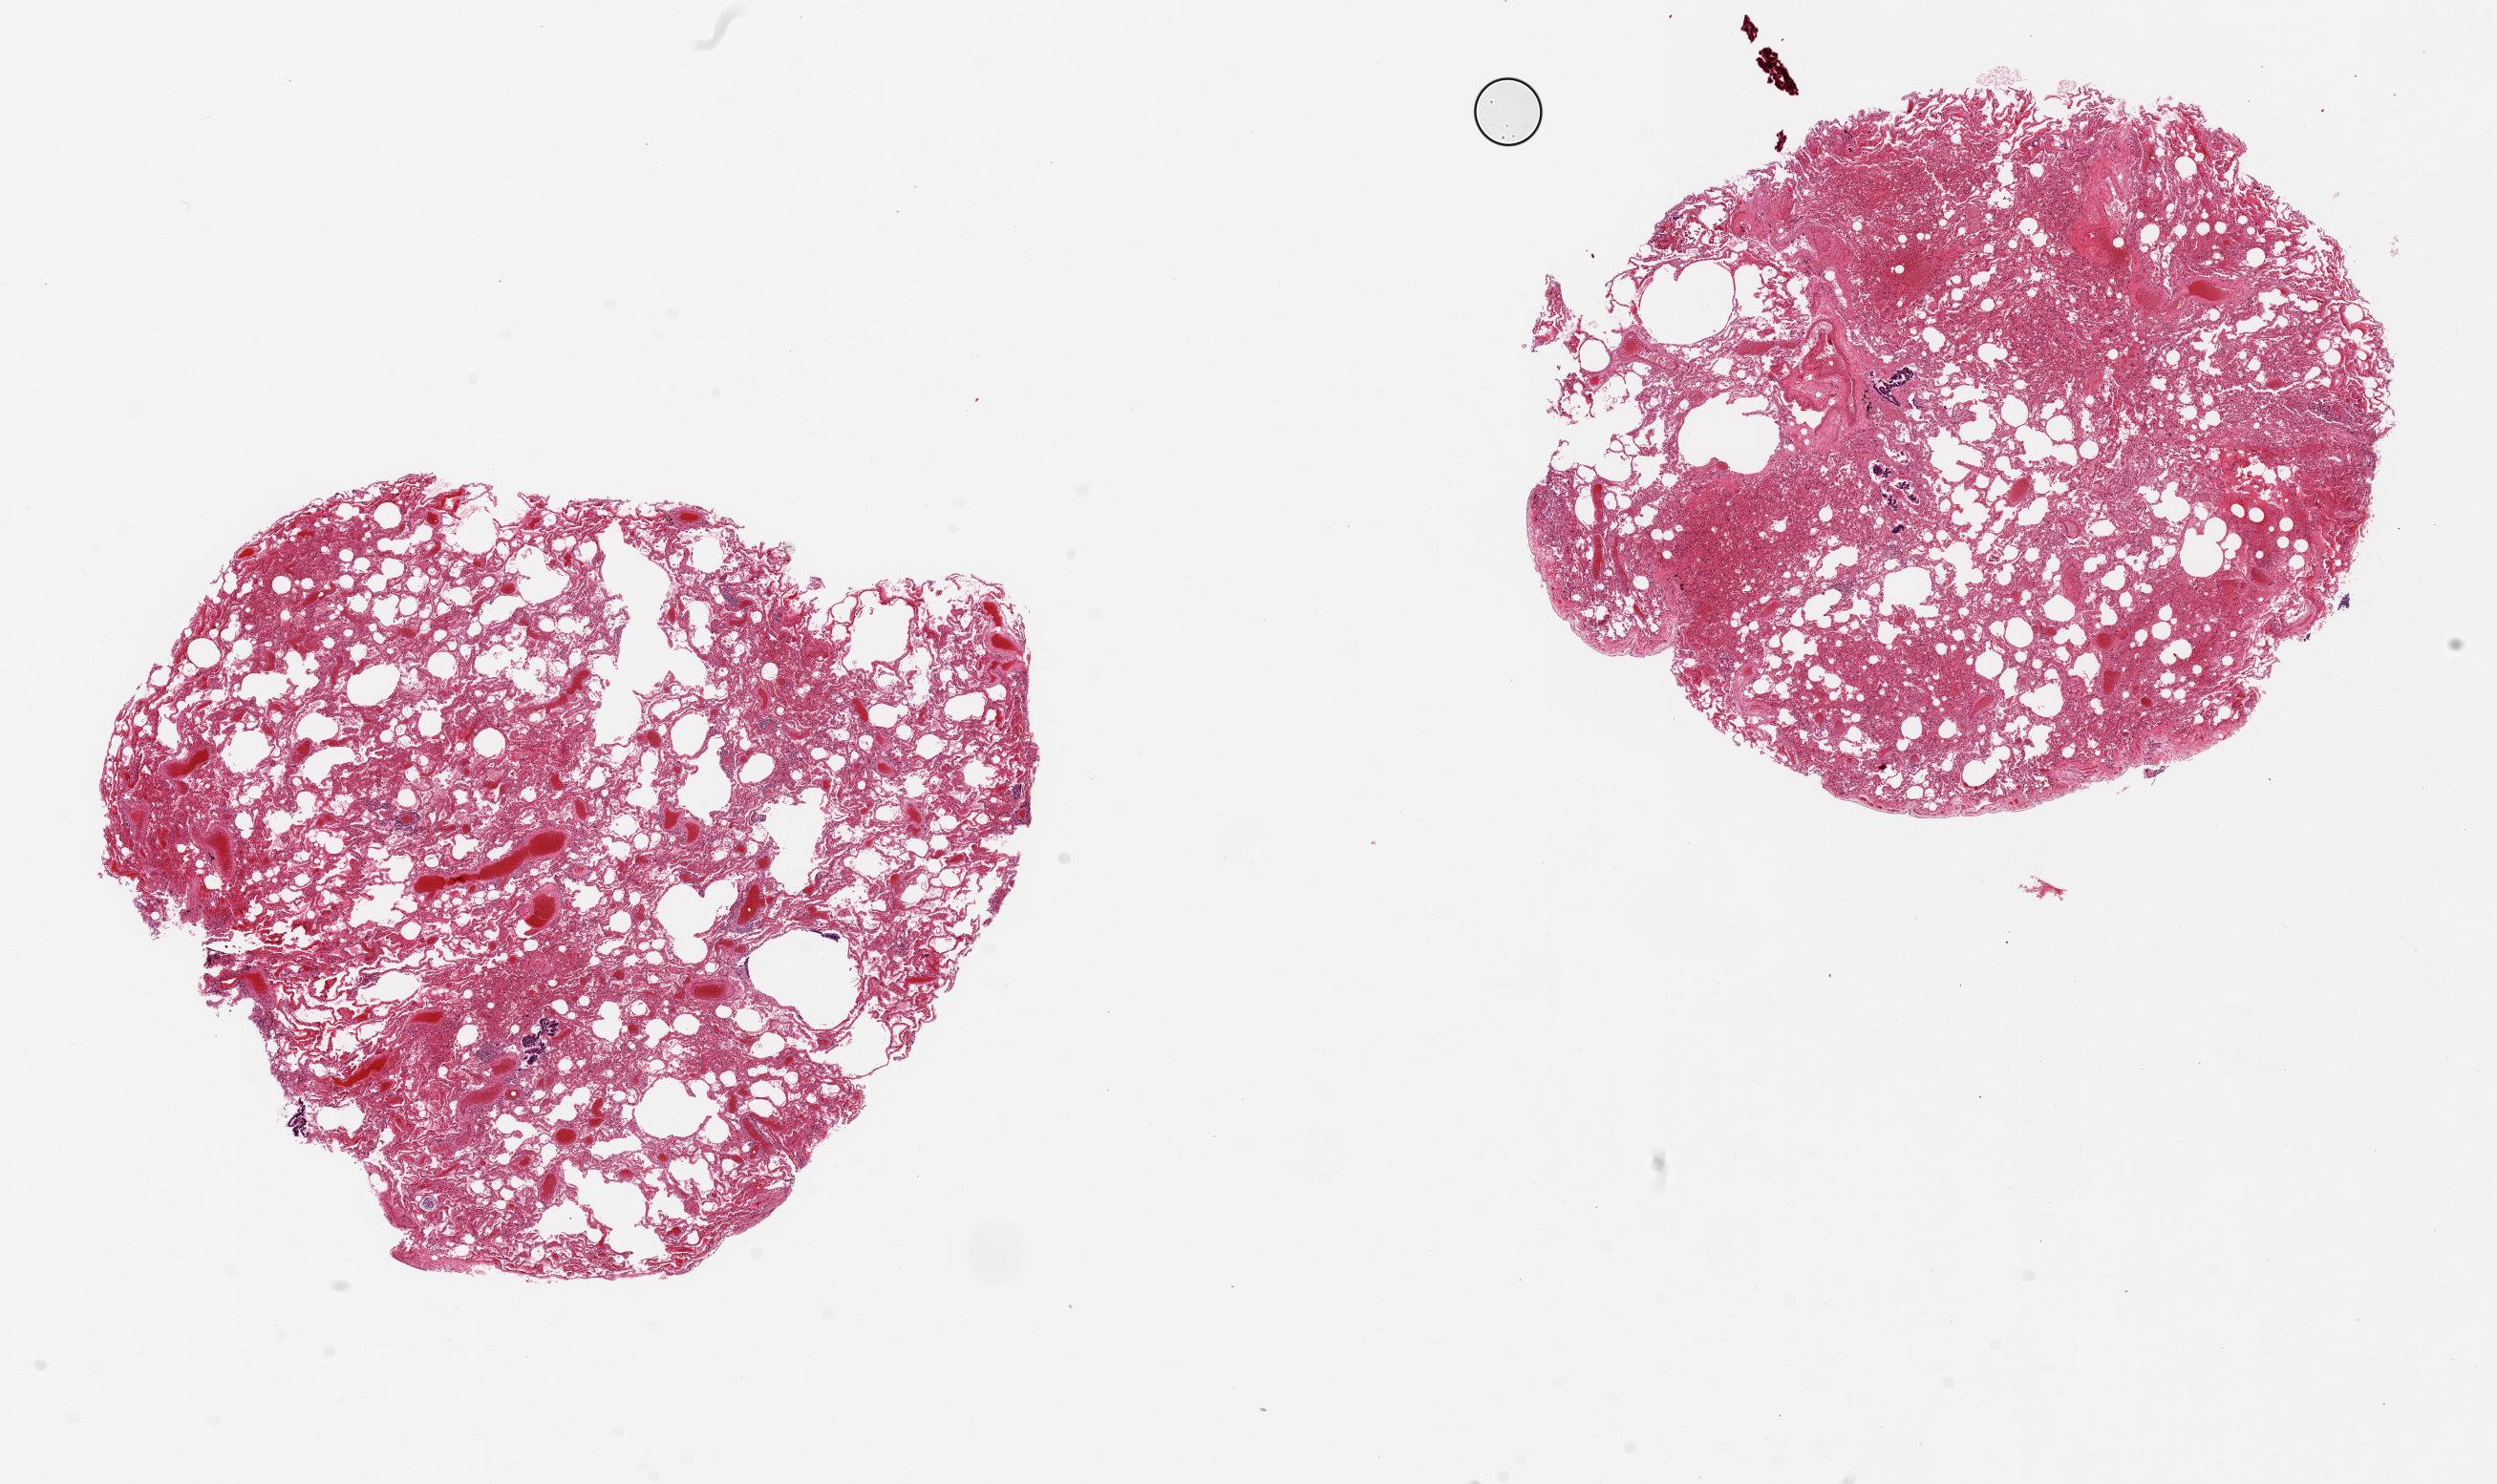
Whole-slide image, H&E stain, a low-resolution overview of the entire scanned area, about 20.7 x 12.3 mm (slide scanned at 20x). PAXgene-fixed, paraffin-embedded tissue. Section of lung (target tissue). Donor tissue sample. Donor: male.
Review note (as recorded): 2 pieces ~7x6mm, diffuse patchy congestion, moderately poorly preserved; degenerating foci of bronchial mucosa.